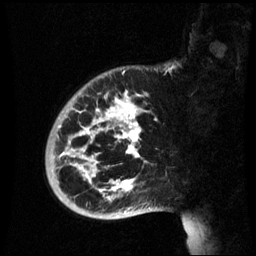
Breast MRI (dynamic contrast-enhanced), one sagittal slice; position 14 of 60 along the scan axis; dynamic contrast-enhanced series, image 2 of 3 at this slice position (ordered by acquisition); 1.5 T; TE 4.2 ms, TR 8.9 ms; 2.6 mm slice thickness; 256 × 256 image matrix. Patient: female, 35 years. From the clinical record (not read from this slice): setting: breast cancer imaged before/during neoadjuvant chemotherapy; receptor status: HR-positive, HER2-negative.
Structures marked on this image (semi-automatically segmented with operator editing):
- analysis volume of interest (the breast-tissue region the enhancement analysis was run in; not a lesion): bounding box (x1, y1, x2, y2) in pixels: (45, 74, 164, 221)
- tumour enhancement mask (voxels above the 70 % enhancement threshold inside the analysis volume of interest): (60, 92, 141, 201)